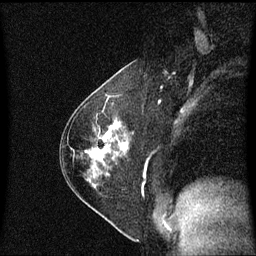
Breast MRI (dynamic contrast-enhanced), one sagittal slice. Slice 35 of 60 in the series (ordered by position). Dynamic contrast-enhanced series, image 2 of 3 at this slice position (ordered by acquisition). 1.5 T. TE 4.2 ms, TR 8.4 ms. 256 × 256 image matrix, field of view 210 × 210 mm. Patient: female, 54 years. Case-level facts recorded for this patient, not image findings: setting: breast cancer imaged before/during neoadjuvant chemotherapy; receptor status: HER2-positive.
Outlined on this slice (semi-automatic segmentation, software-assisted and operator-edited):
- analysis volume of interest (the breast-tissue region the enhancement analysis was run in; not a lesion): bounding box (x1, y1, x2, y2) in pixels: (87, 123, 130, 188)
- tumour enhancement mask (voxels above the 70 % enhancement threshold inside the analysis volume of interest): (107, 133, 128, 151)